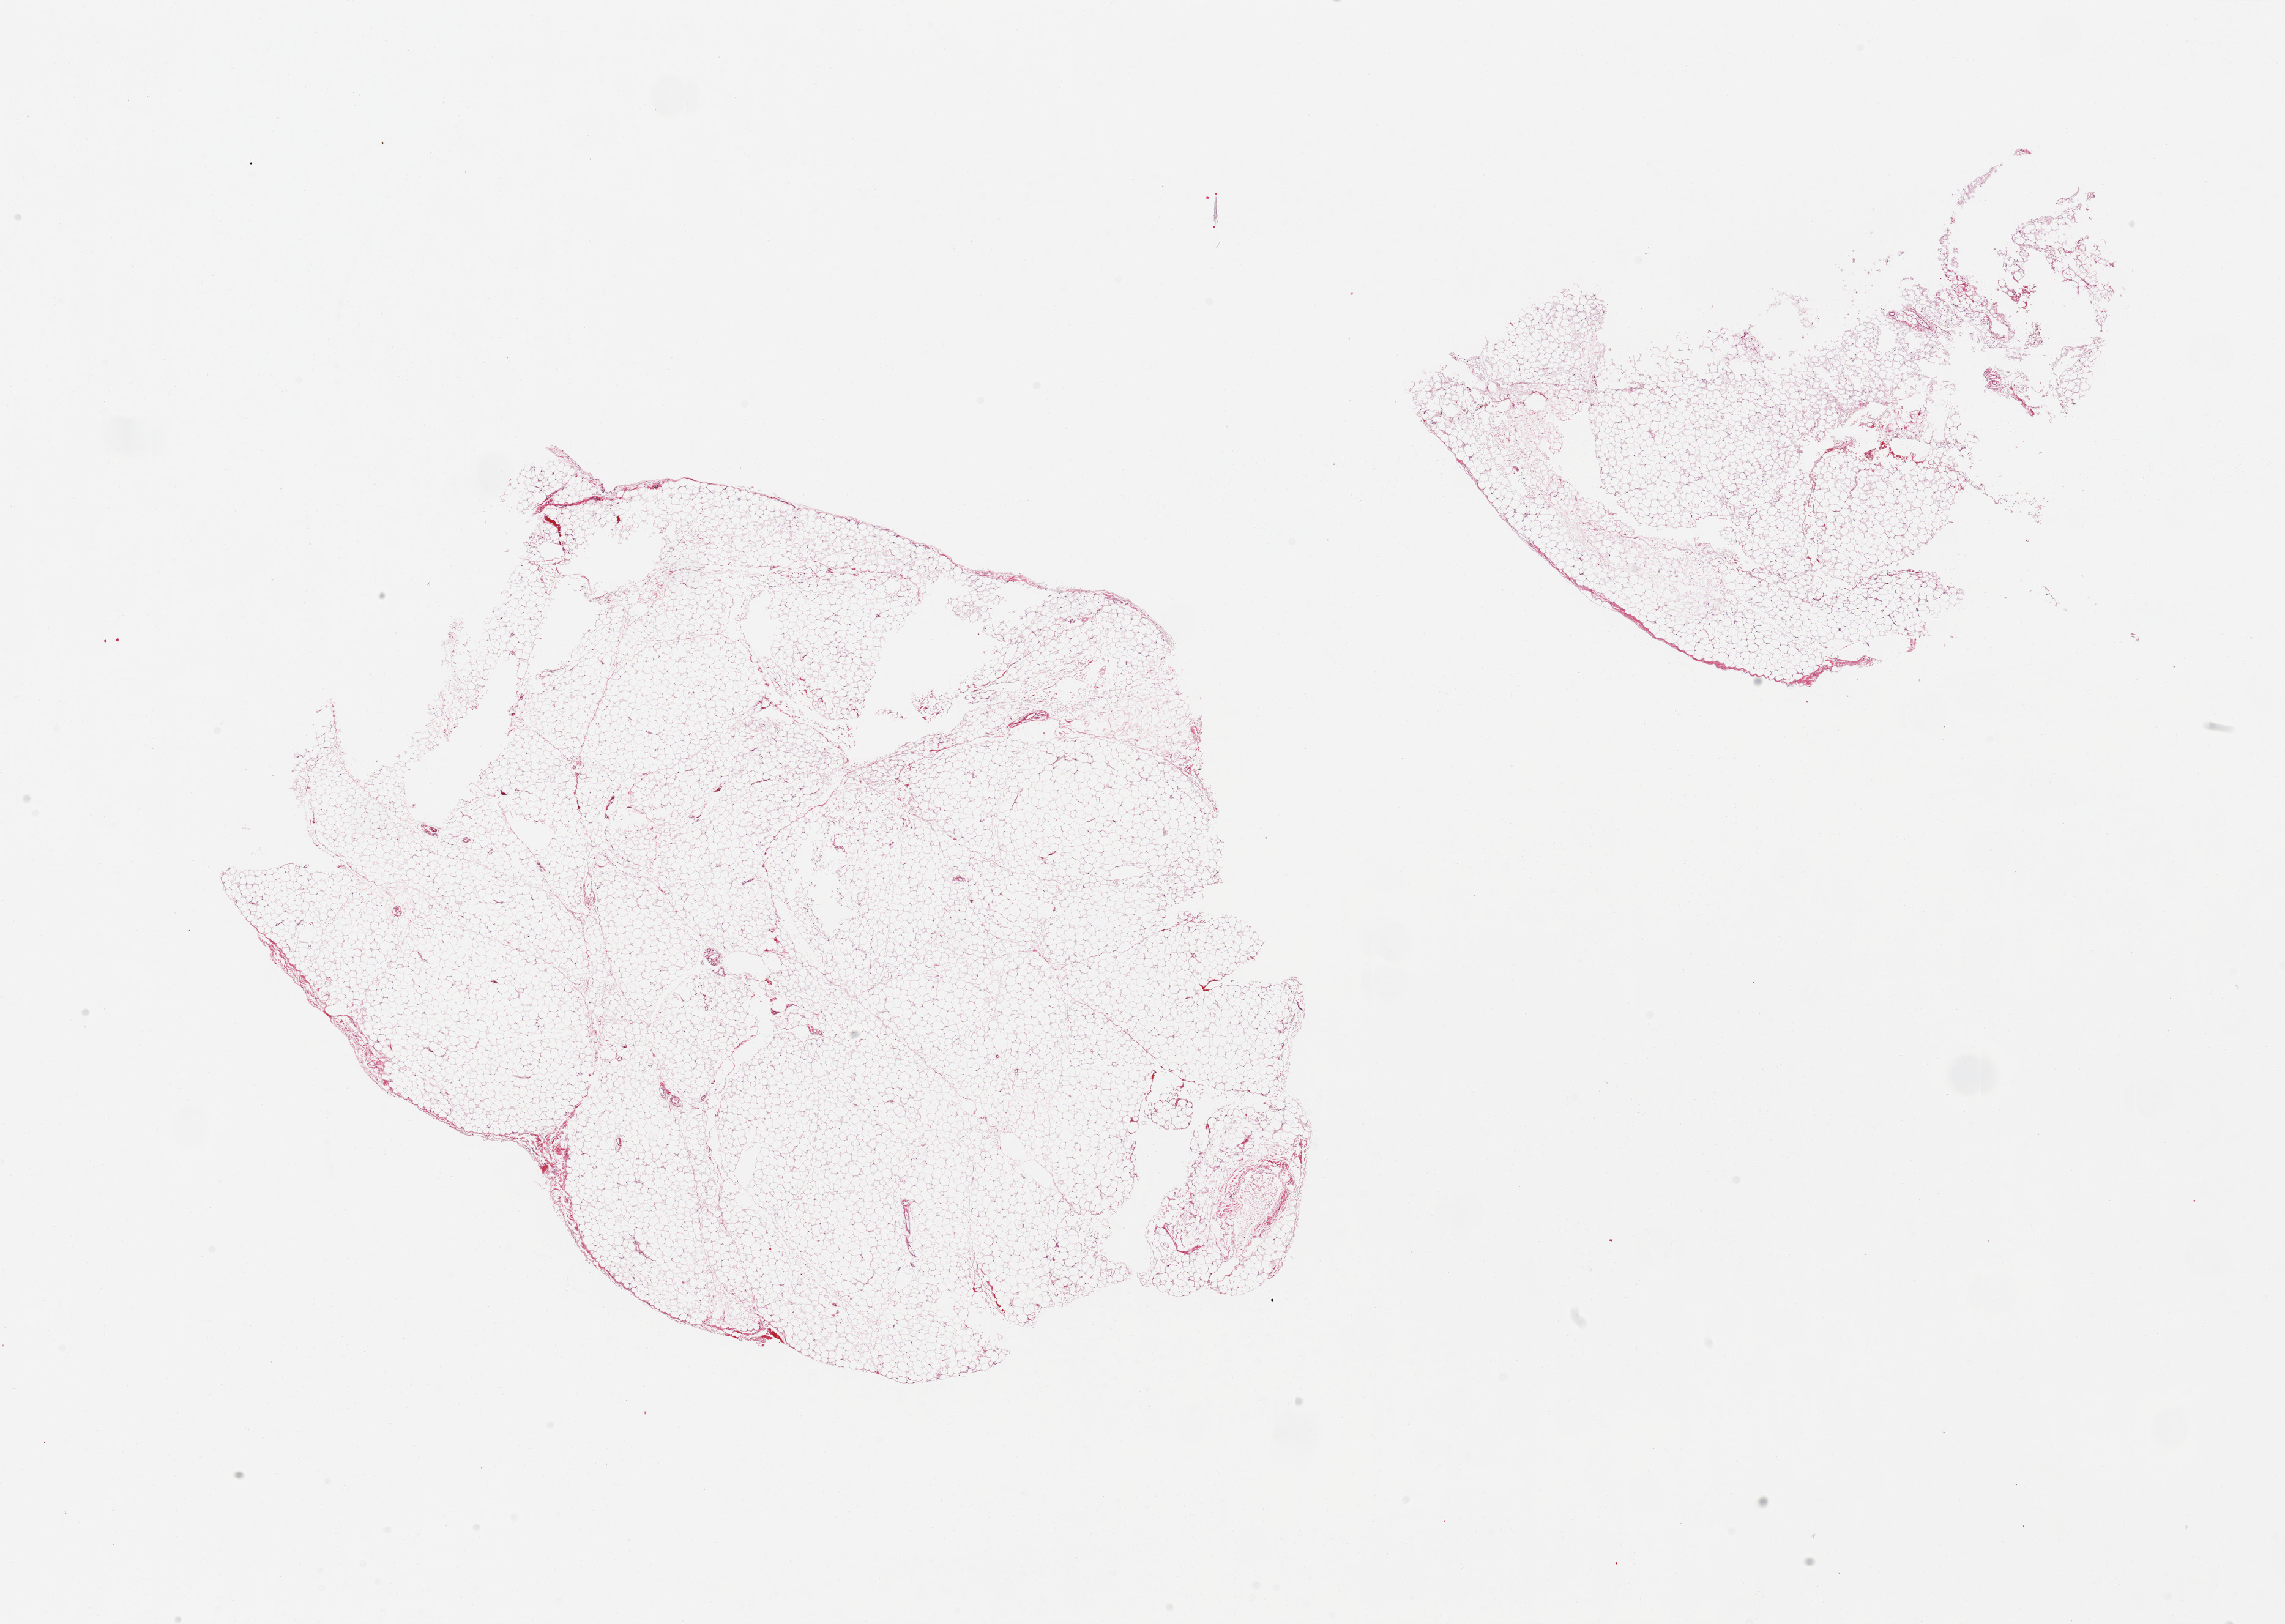
Digitized haematoxylin and eosin-stained section — shown as a low-resolution overview of the whole scanned area (about 29.5 x 21.0 mm, acquisition: 20x scan), PAXgene-fixed paraffin-embedded (PFPE) section, sampled site (target tissue): omentum, tissue donor sample.
Review note (as recorded): 2 pieces.